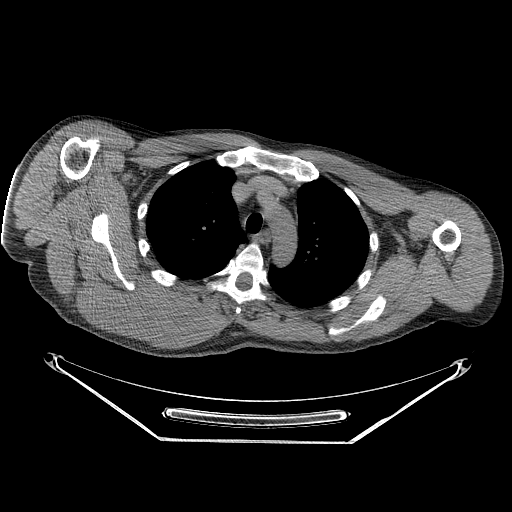
CT of an extremity soft-tissue mass (from a PET/CT study), one axial slice. Position 189 of 267 along the scan axis. Reconstruction kernel STANDARD. 140 kVp. Soft-tissue window (W 400 / L 40 HU). 512 × 512 image matrix. Male patient. Case-level facts recorded for this patient, not image findings: histological type: pleiomorphic spindle cell undifferentiated; grade: high; site of the primary tumour: right parascapusular.
Structures marked on this image (expert contour drawn on MRI and transferred to this co-registered scan by the dataset authors):
- gross tumour volume including surrounding oedema: box from (x=80, y=267) to (x=222, y=337) px
- gross tumour volume (mass): (x=80, y=267)–(x=204, y=334)